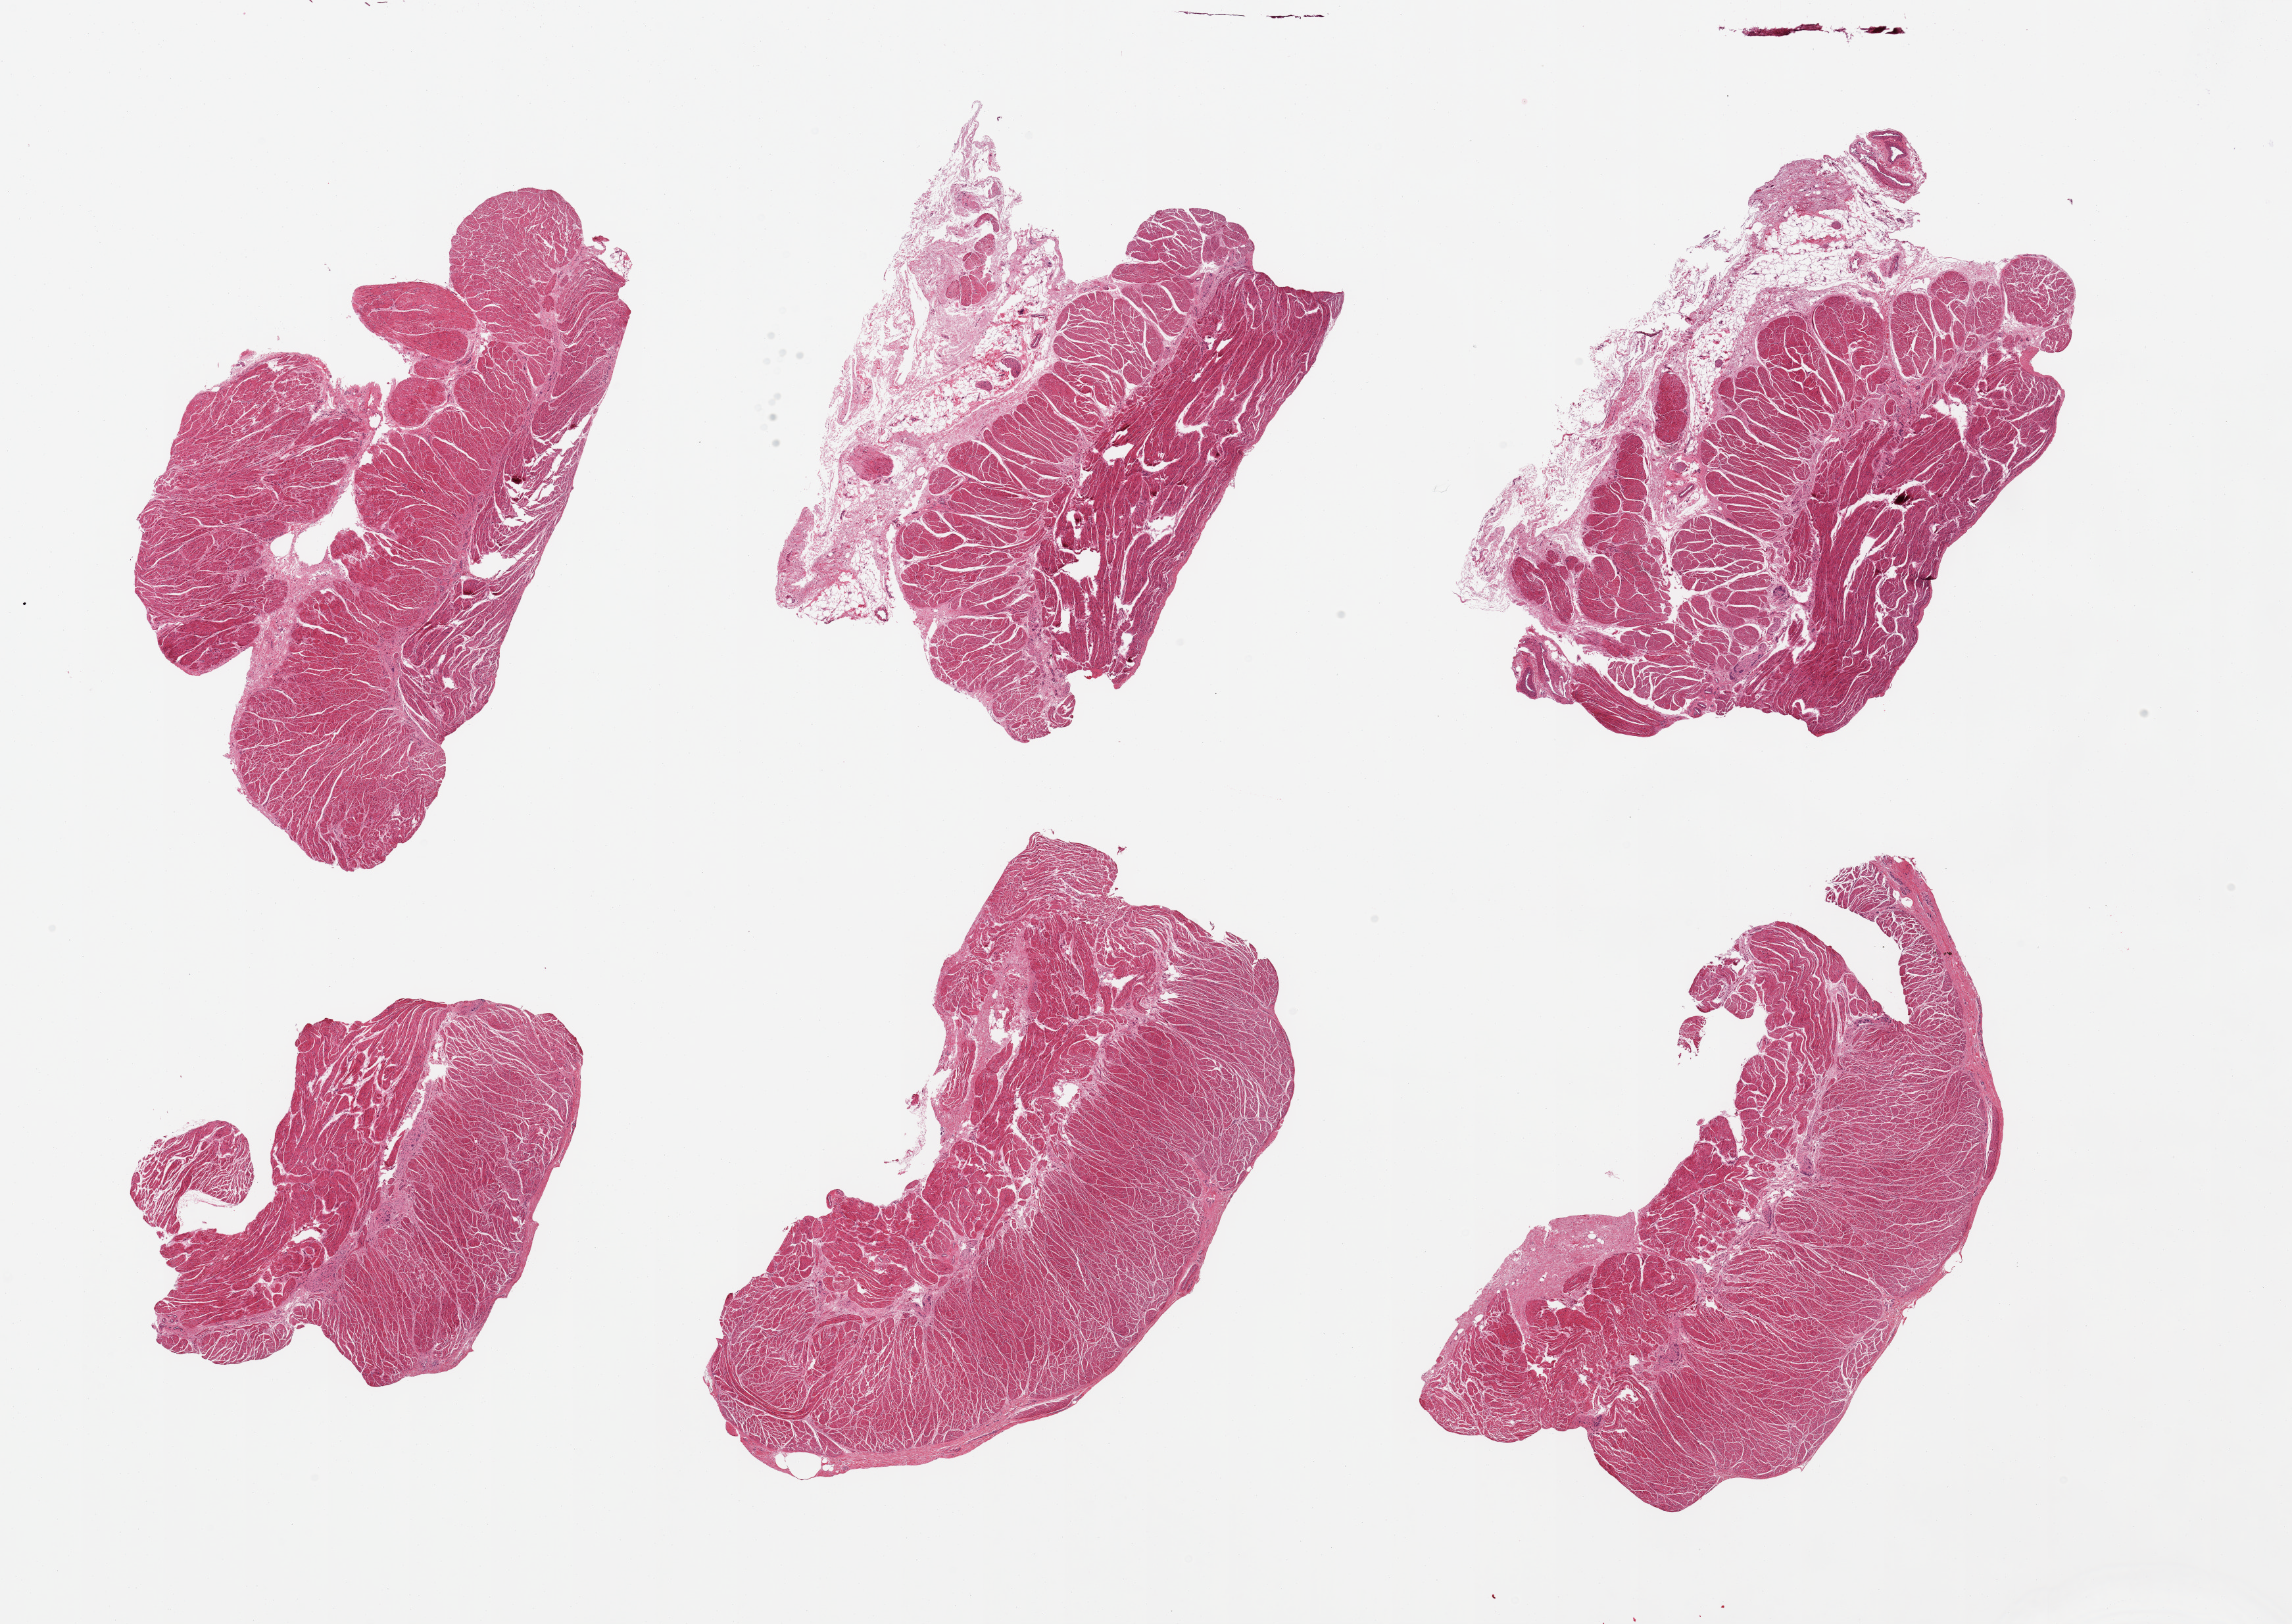
H&E whole-slide image, whole scanned area (about 27.6 x 19.5 mm, slide scanned at 20x) shown as a low-resolution overview, PAXgene-fixed, paraffin-embedded tissue, sampled site (target tissue): gastroesophageal junction, donor tissue sample. Male donor.
Pathologist's review note for this sample: 6 pieces; 2 pieces have up to 30% submucosal fibrofatty tissue.